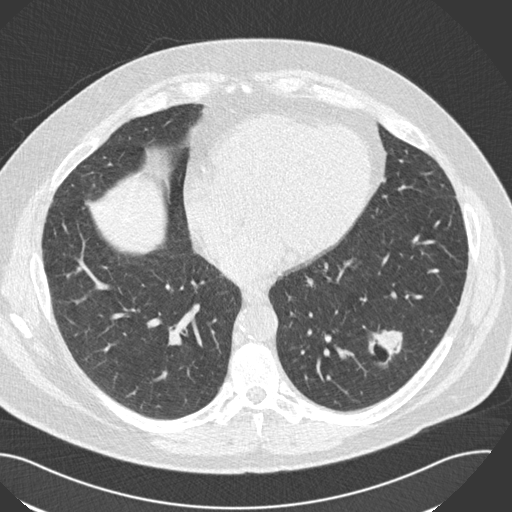
Axial slice from a low-dose chest CT screening exam. Third screening round (two years after baseline). Lung window (W 1500 / L -600 HU). 2 mm slice thickness. Standard (soft-tissue) reconstruction kernel (B30f). 120 kVp. Slice 84 of 153 in the series. 512 × 512 image matrix. Male participant, aged 57 years at enrolment.
• Lesion marked by an expert reader, box from (x=349, y=316) to (x=419, y=373) px.
• The exam's reader record, not a measurement of the box and not confirmed to be the same lesion: non-calcified nodule or mass ≥4 mm, left lower lobe, 22 × 18 mm, poorly defined margins, soft tissue attenuation, pre-existing on the prior screen: yes; interval growth: yes.
• Participant outcome: lung cancer diagnosed 124 days after this screen — squamous cell carcinoma, NOS, left lower lobe, moderately differentiated (G2), stage IA (AJCC 6th edition), 22 mm at pathology.